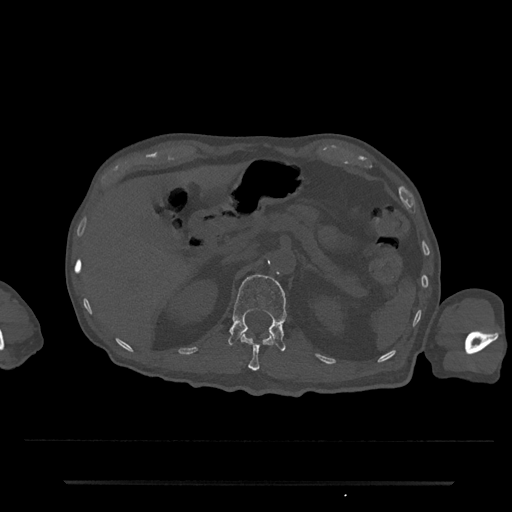
CT including the spine, one axial slice. Slice 154 of 797 in the series (ordered by position). 120 kVp. Bone window (W 1800 / L 400 HU). 512 × 512 image matrix, field of view 427 × 427 mm. Patient: male, 74 years. Case-level facts recorded for this patient, not image findings: primary cancer: prostate.
Annotated regions visible in this slice (semi-automatically segmented with operator editing):
- L1 vertebra: box from (x=228, y=274) to (x=287, y=352) px
- T12 vertebra: (x=240, y=333)–(x=273, y=371)